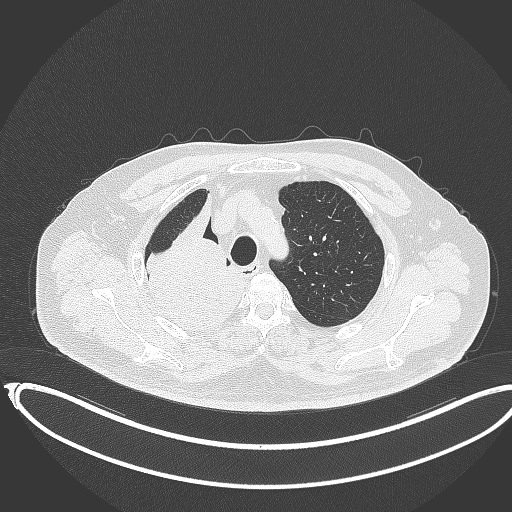
Chest CT, one axial slice; slice 292 of 403 in the series (ordered by position); reconstruction kernel B70f; 120 kVp; lung window (W 1500 / L -600 HU); 1 mm slice thickness; 512 × 512 image matrix, field of view 436 × 436 mm. Patient: male, 68 years. Case-level facts recorded for this patient, not image findings: clinical TNM (as recorded): T2a N0 M0.
Annotated regions visible in this slice (bounding box drawn by a radiologist):
- lung tumour (recorded histology: adenocarcinoma): bounding box [x1, y1, x2, y2] px = [130, 190, 244, 341]